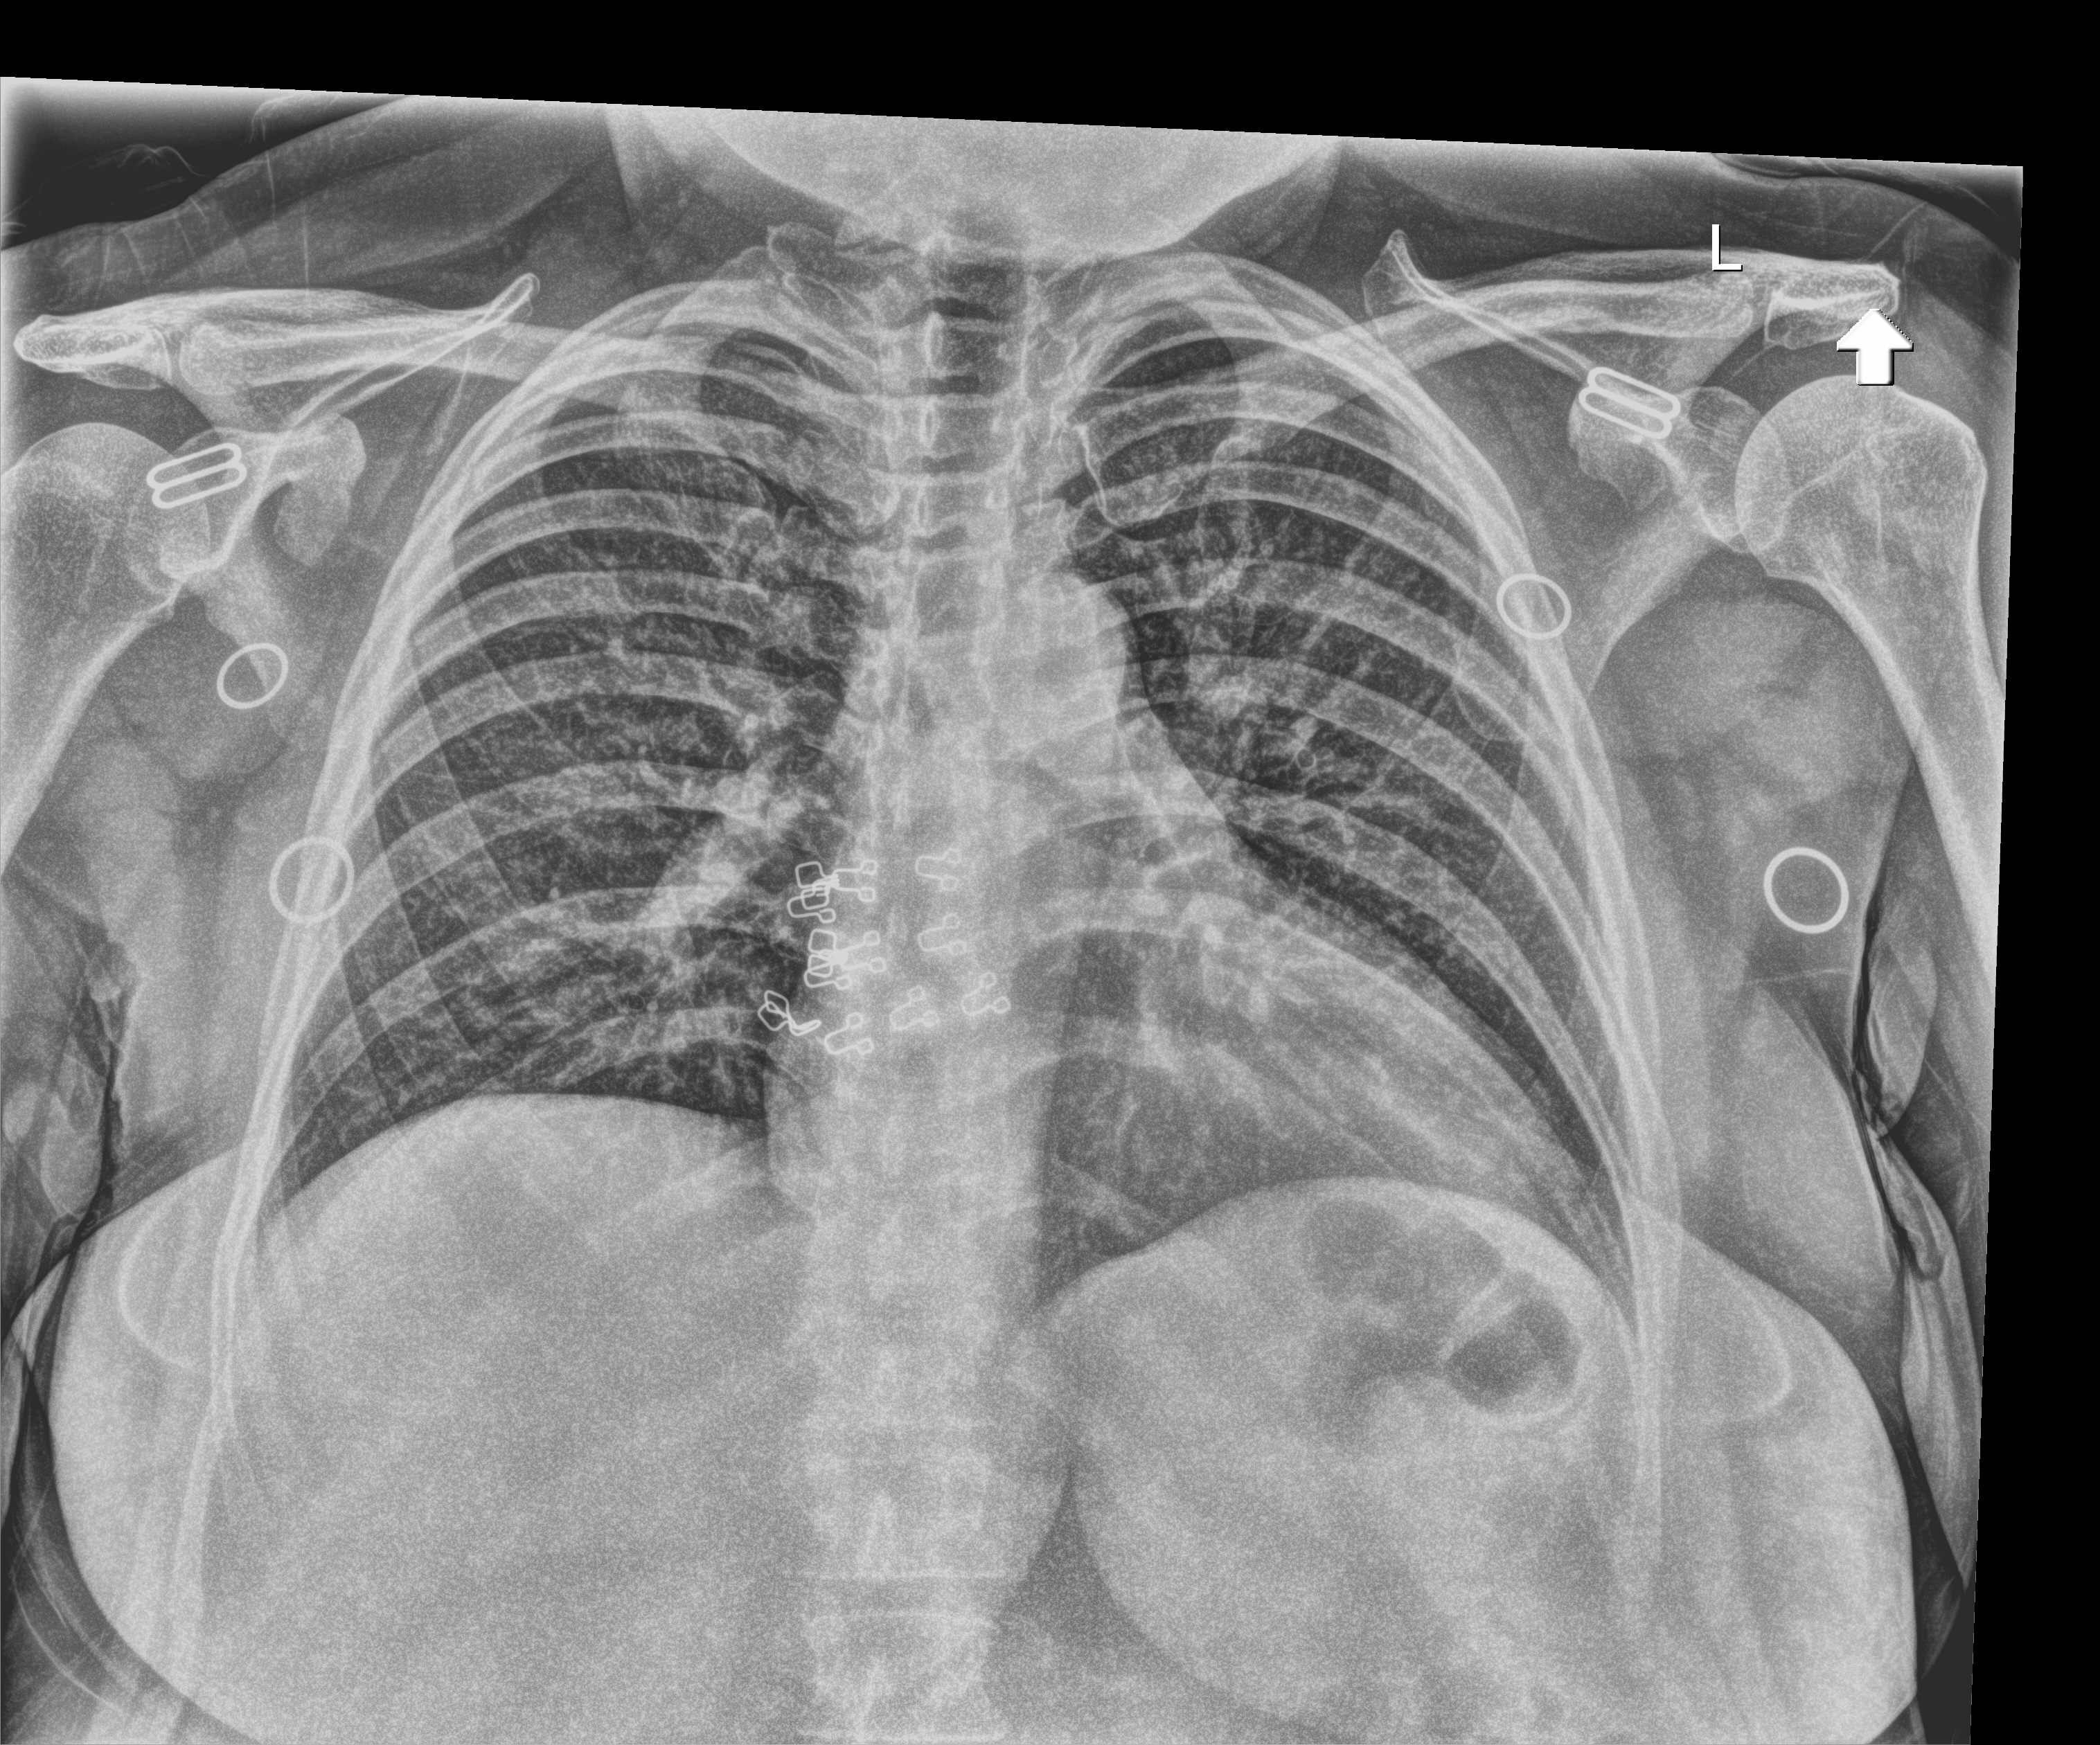
Bedside chest radiograph (digital radiography). Patient hospitalised with COVID-19; female, aged 18–59 years.
Admission-level facts for this patient (not findings on this image; timing relative to this image not recorded): admitted to intensive care during this hospital stay: no; COPD (admission record): no; mechanically ventilated during this hospital stay: no.